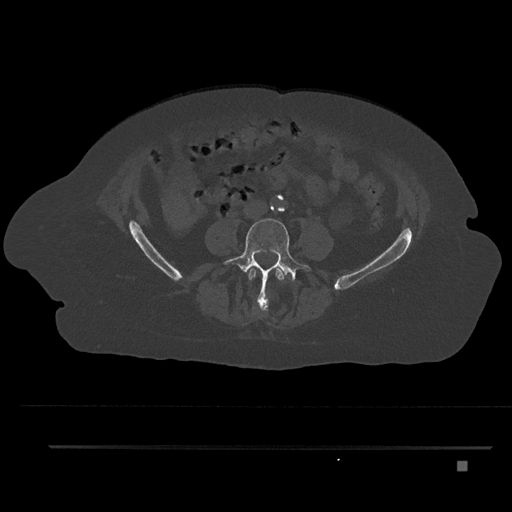
CT including the spine, one axial slice. Slice 87 of 797 in the series (ordered by position). Reconstruction kernel Br40s/3. 120 kVp. Bone window (W 1800 / L 400 HU). 0.5 mm slice thickness. 512 × 512 image matrix, field of view 437 × 437 mm. Patient: female, 76 years. Case-level facts recorded for this patient, not image findings: primary cancer: lung; vertebrae with lytic lesions (as recorded): T11, L3.
Annotated regions visible in this slice (semi-automatic segmentation, software-assisted and operator-edited):
- L3 vertebra: bounding box <248,267,285,311> (left, top, right, bottom; pixels)
- L4 vertebra: <222,218,311,311>